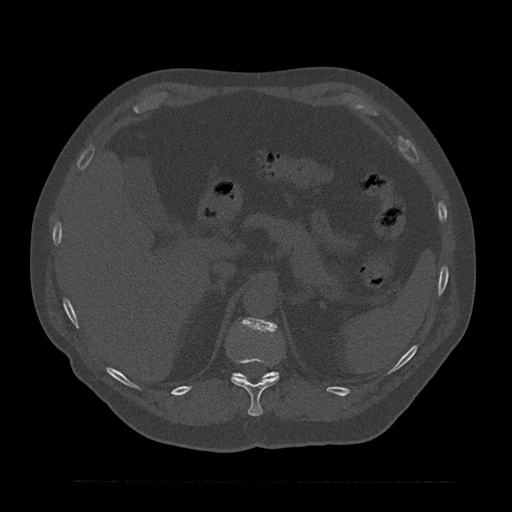
CT including the spine, one axial slice; position 270 of 797 along the scan axis; reconstruction kernel Br40s/3; 120 kVp; bone window (W 1800 / L 400 HU); 0.5 mm slice thickness; 512 × 512 image matrix, field of view 430 × 430 mm. Male patient, age 61 years. Case-level facts recorded for this patient, not image findings: primary cancer: prostate.
Outlined on this slice (semi-automatically segmented with operator editing):
- T11 vertebra: bounding box (x1, y1, x2, y2) in pixels: (231, 357, 279, 416)
- T12 vertebra: (234, 319, 279, 379)